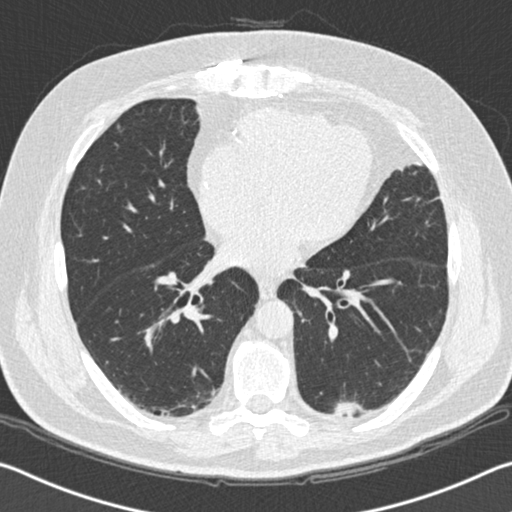
Low-dose screening chest CT, one axial slice; slice 79 of 172 in the series (ordered by position); lung window (W 1500 / L -600 HU); 2 mm slice thickness; 512 × 512 image matrix, field of view 340 × 340 mm.
Outlined on this slice (expert manual segmentation):
- lesion 1 (tumor, lower lobe of left lung): bounding box (x1, y1, x2, y2) in pixels: (334, 400, 366, 417)